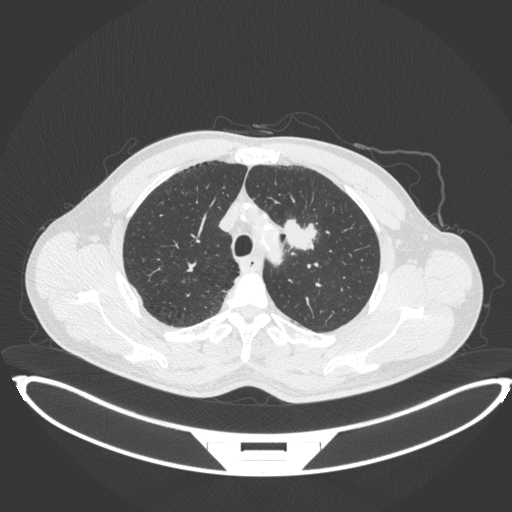
Chest CT, one axial slice. Position 339 of 407 along the scan axis. 120 kVp. Lung window (W 1500 / L -600 HU). 512 × 512 image matrix. Patient: male, 60 years. From the clinical record (not read from this slice): clinical TNM (as recorded): T2a N0 M0; histopathological grade: G1-G2.
Structures marked on this image (rectangle marked by the reading radiologist):
- lung tumour (recorded histology: squamous cell carcinoma): bounding box (x1, y1, x2, y2) in pixels: (280, 216, 317, 252)